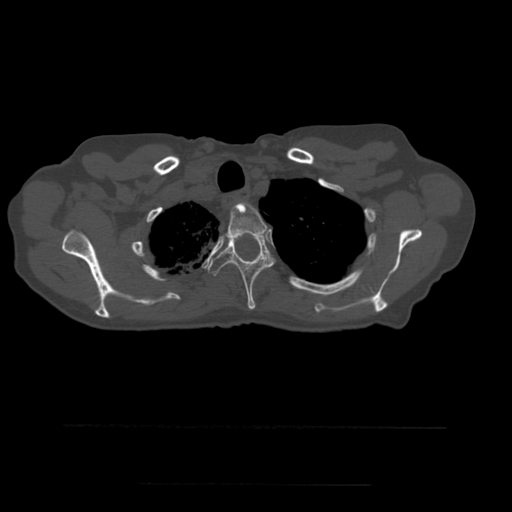
CT including the spine, one axial slice. Position 425 of 544 along the scan axis. Bone window (W 1800 / L 400 HU). 1.25 mm slice thickness. 512 × 512 image matrix. Patient age 58 years. From the clinical record (not read from this slice): primary cancer: lung.
Outlined on this slice (semi-automatically segmented with operator editing):
- T2 vertebra: bounding box <225,203,267,239> (left, top, right, bottom; pixels)
- T3 vertebra: <208,235,274,310>